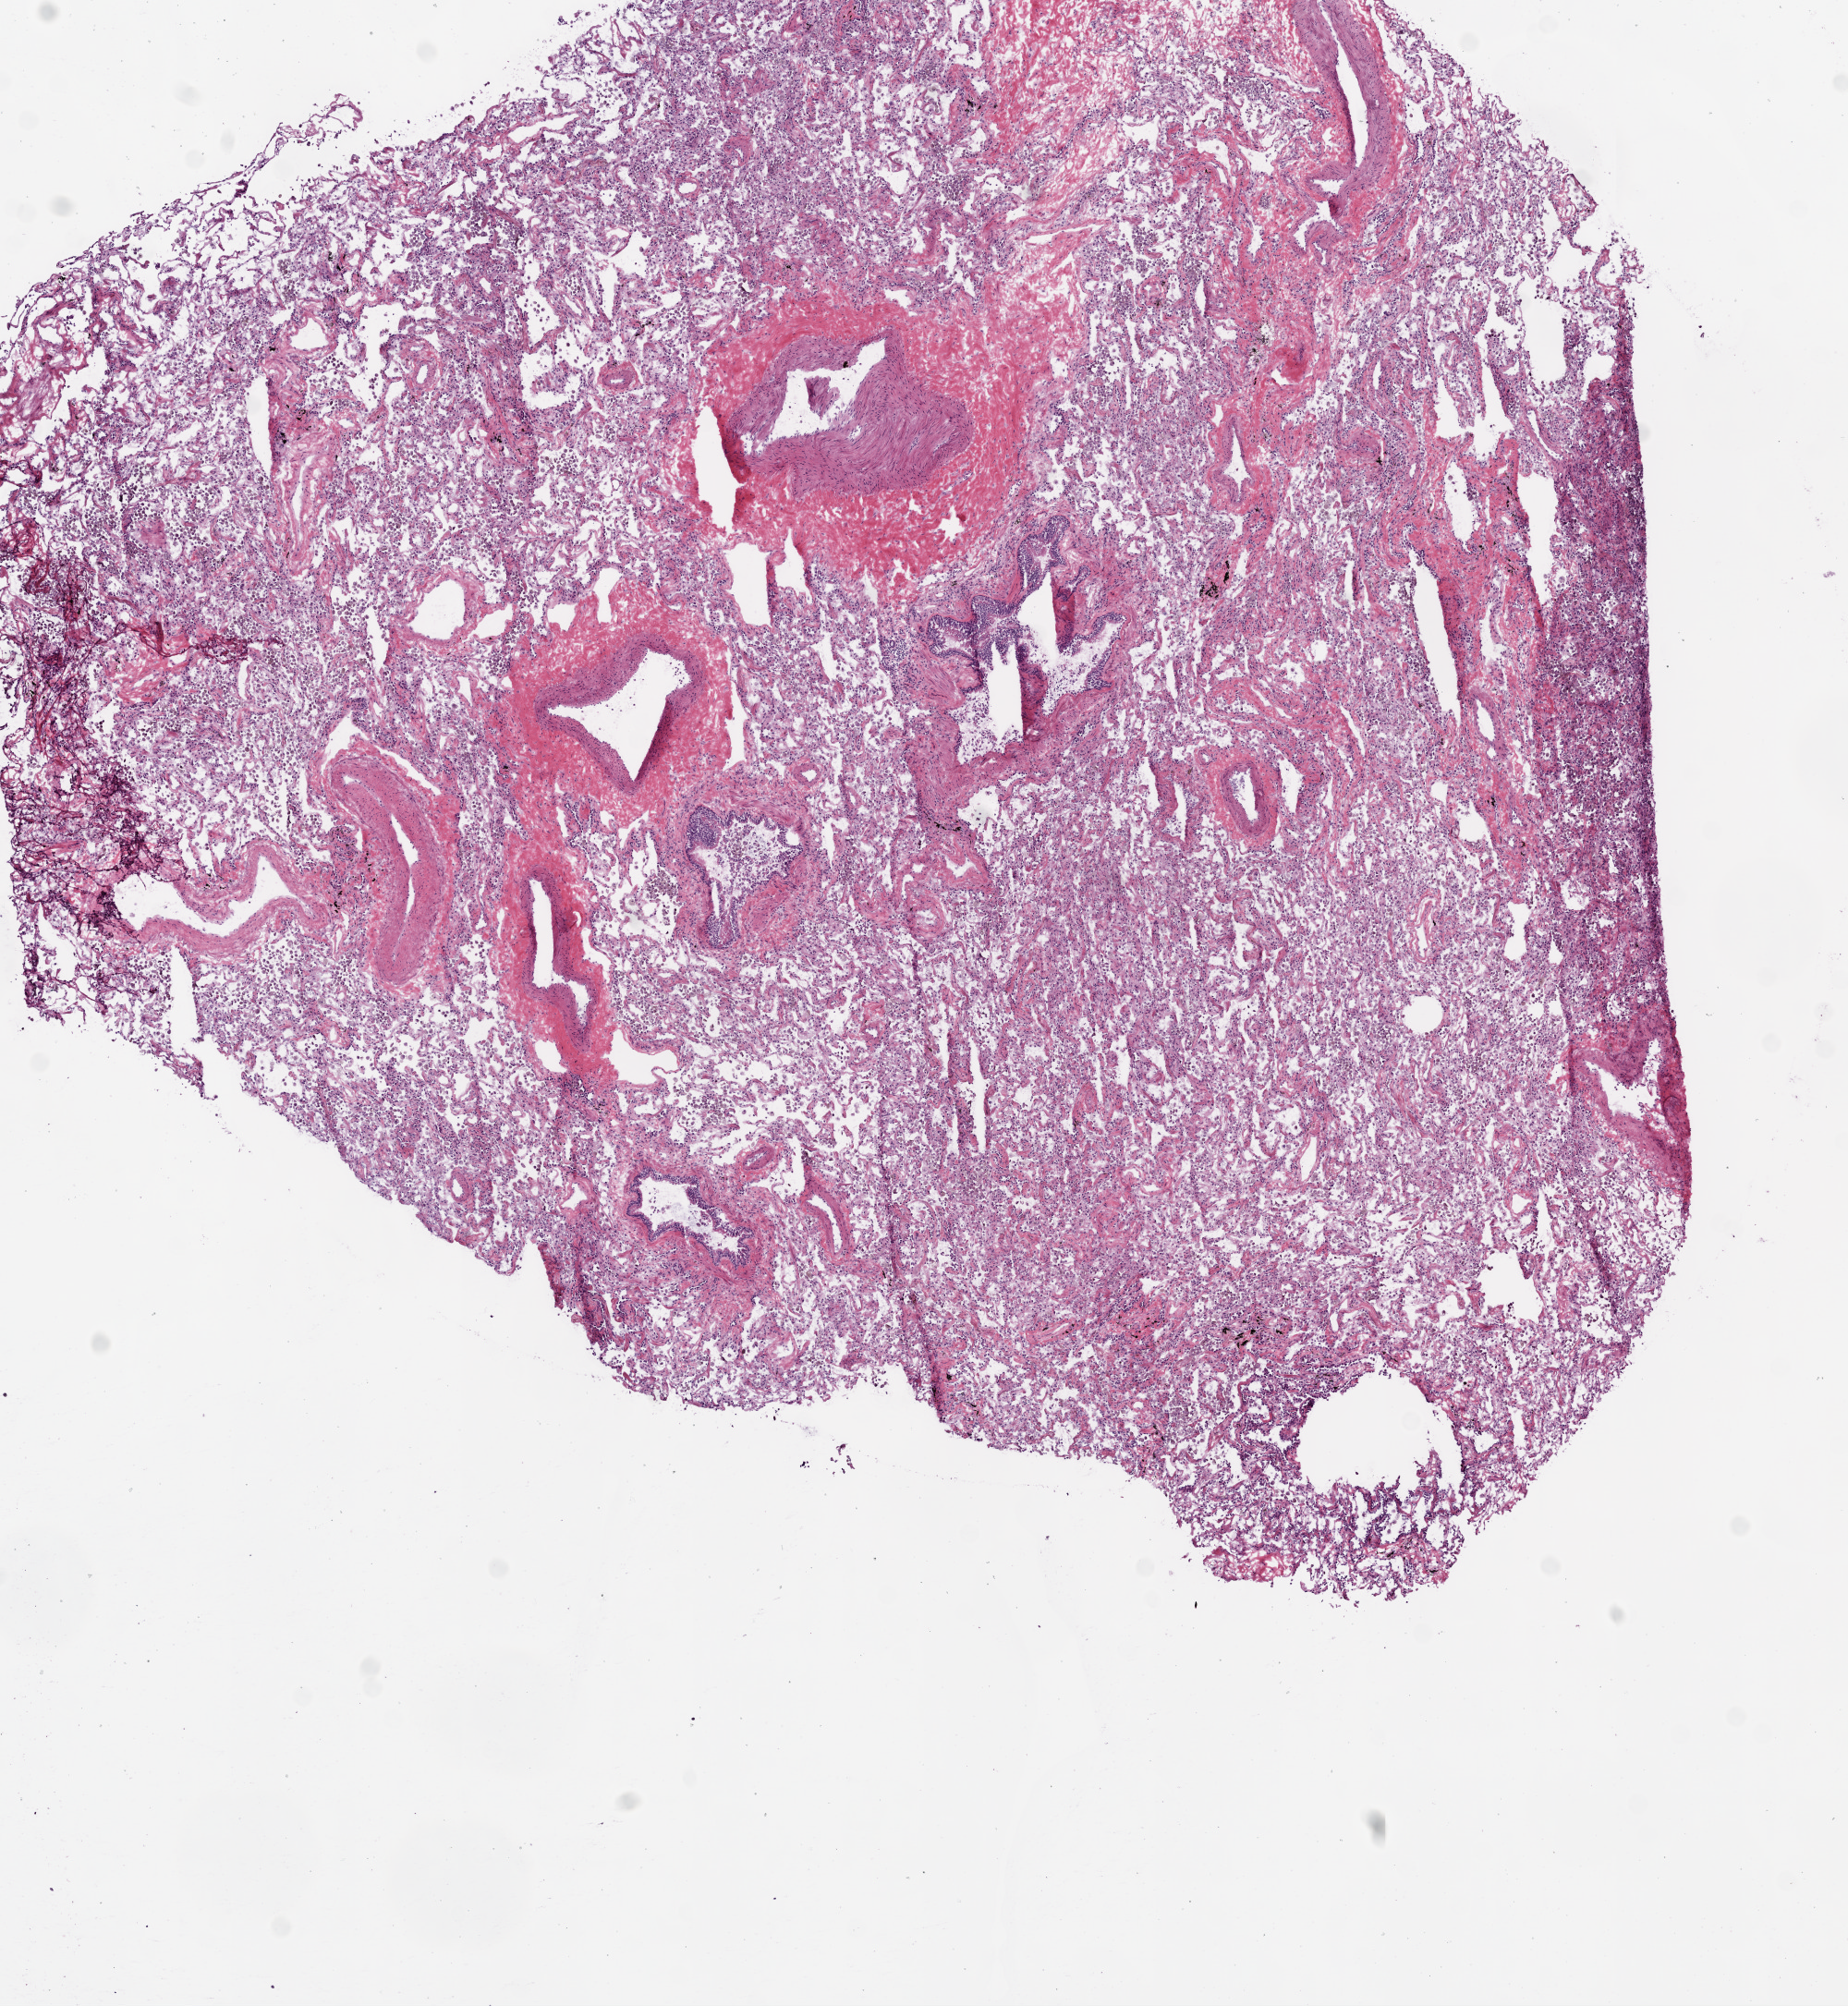
Digitized H&E-stained tissue section (whole slide), a low-resolution overview of the entire scanned area, about 8.0 x 8.7 mm (from a 20x scan); frozen section from the bottom of the tissue portion; lung, solid tissue normal (non-tumour tissue) sample. Patient: female, age at initial diagnosis 66 years.
This section: solid tissue normal (non-tumour) sample from the same patient. Patient diagnosis: Adenocarcinoma, NOS (upper lobe, lung).